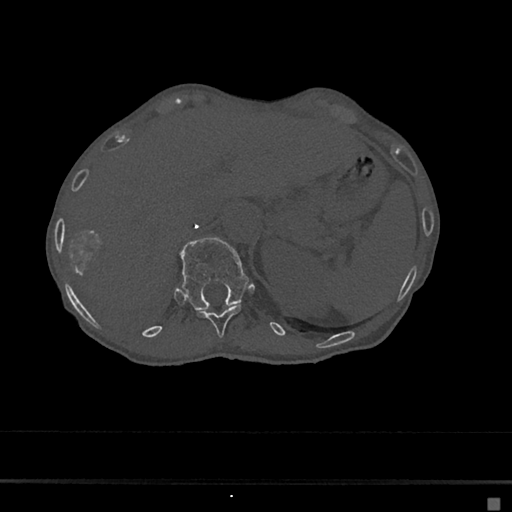
CT including the spine, one axial slice. Slice 142 of 797 in the series (ordered by position). Bone window (W 1800 / L 400 HU). 512 × 512 image matrix. Patient: female, 68 years. From the clinical record (not read from this slice): primary cancer: renal.
Annotated regions visible in this slice (semi-automatic segmentation, software-assisted and operator-edited):
- T11 vertebra: bounding box (x1, y1, x2, y2) in pixels: (196, 304, 243, 337)
- T12 vertebra: (180, 238, 249, 311)